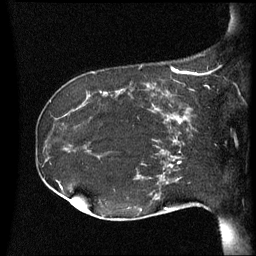
Breast MRI (dynamic contrast-enhanced), one sagittal slice; position 24 of 60 along the scan axis; dynamic contrast-enhanced series, image 2 of 3 at this slice position (ordered by acquisition); 1.5 T; TE 4.2 ms, TR 8.4 ms; 2.5 mm slice thickness; 256 × 256 image matrix, field of view 220 × 220 mm. Patient: female, 41 years. From the clinical record (not read from this slice): setting: breast cancer imaged before/during neoadjuvant chemotherapy; receptor status: HER2-positive.
Annotated regions visible in this slice (semi-automatically segmented with operator editing):
- analysis volume of interest (the breast-tissue region the enhancement analysis was run in; not a lesion): bounding box (x1, y1, x2, y2) in pixels: (122, 84, 195, 137)
- tumour enhancement mask (voxels above the 70 % enhancement threshold inside the analysis volume of interest): (122, 86, 190, 137)